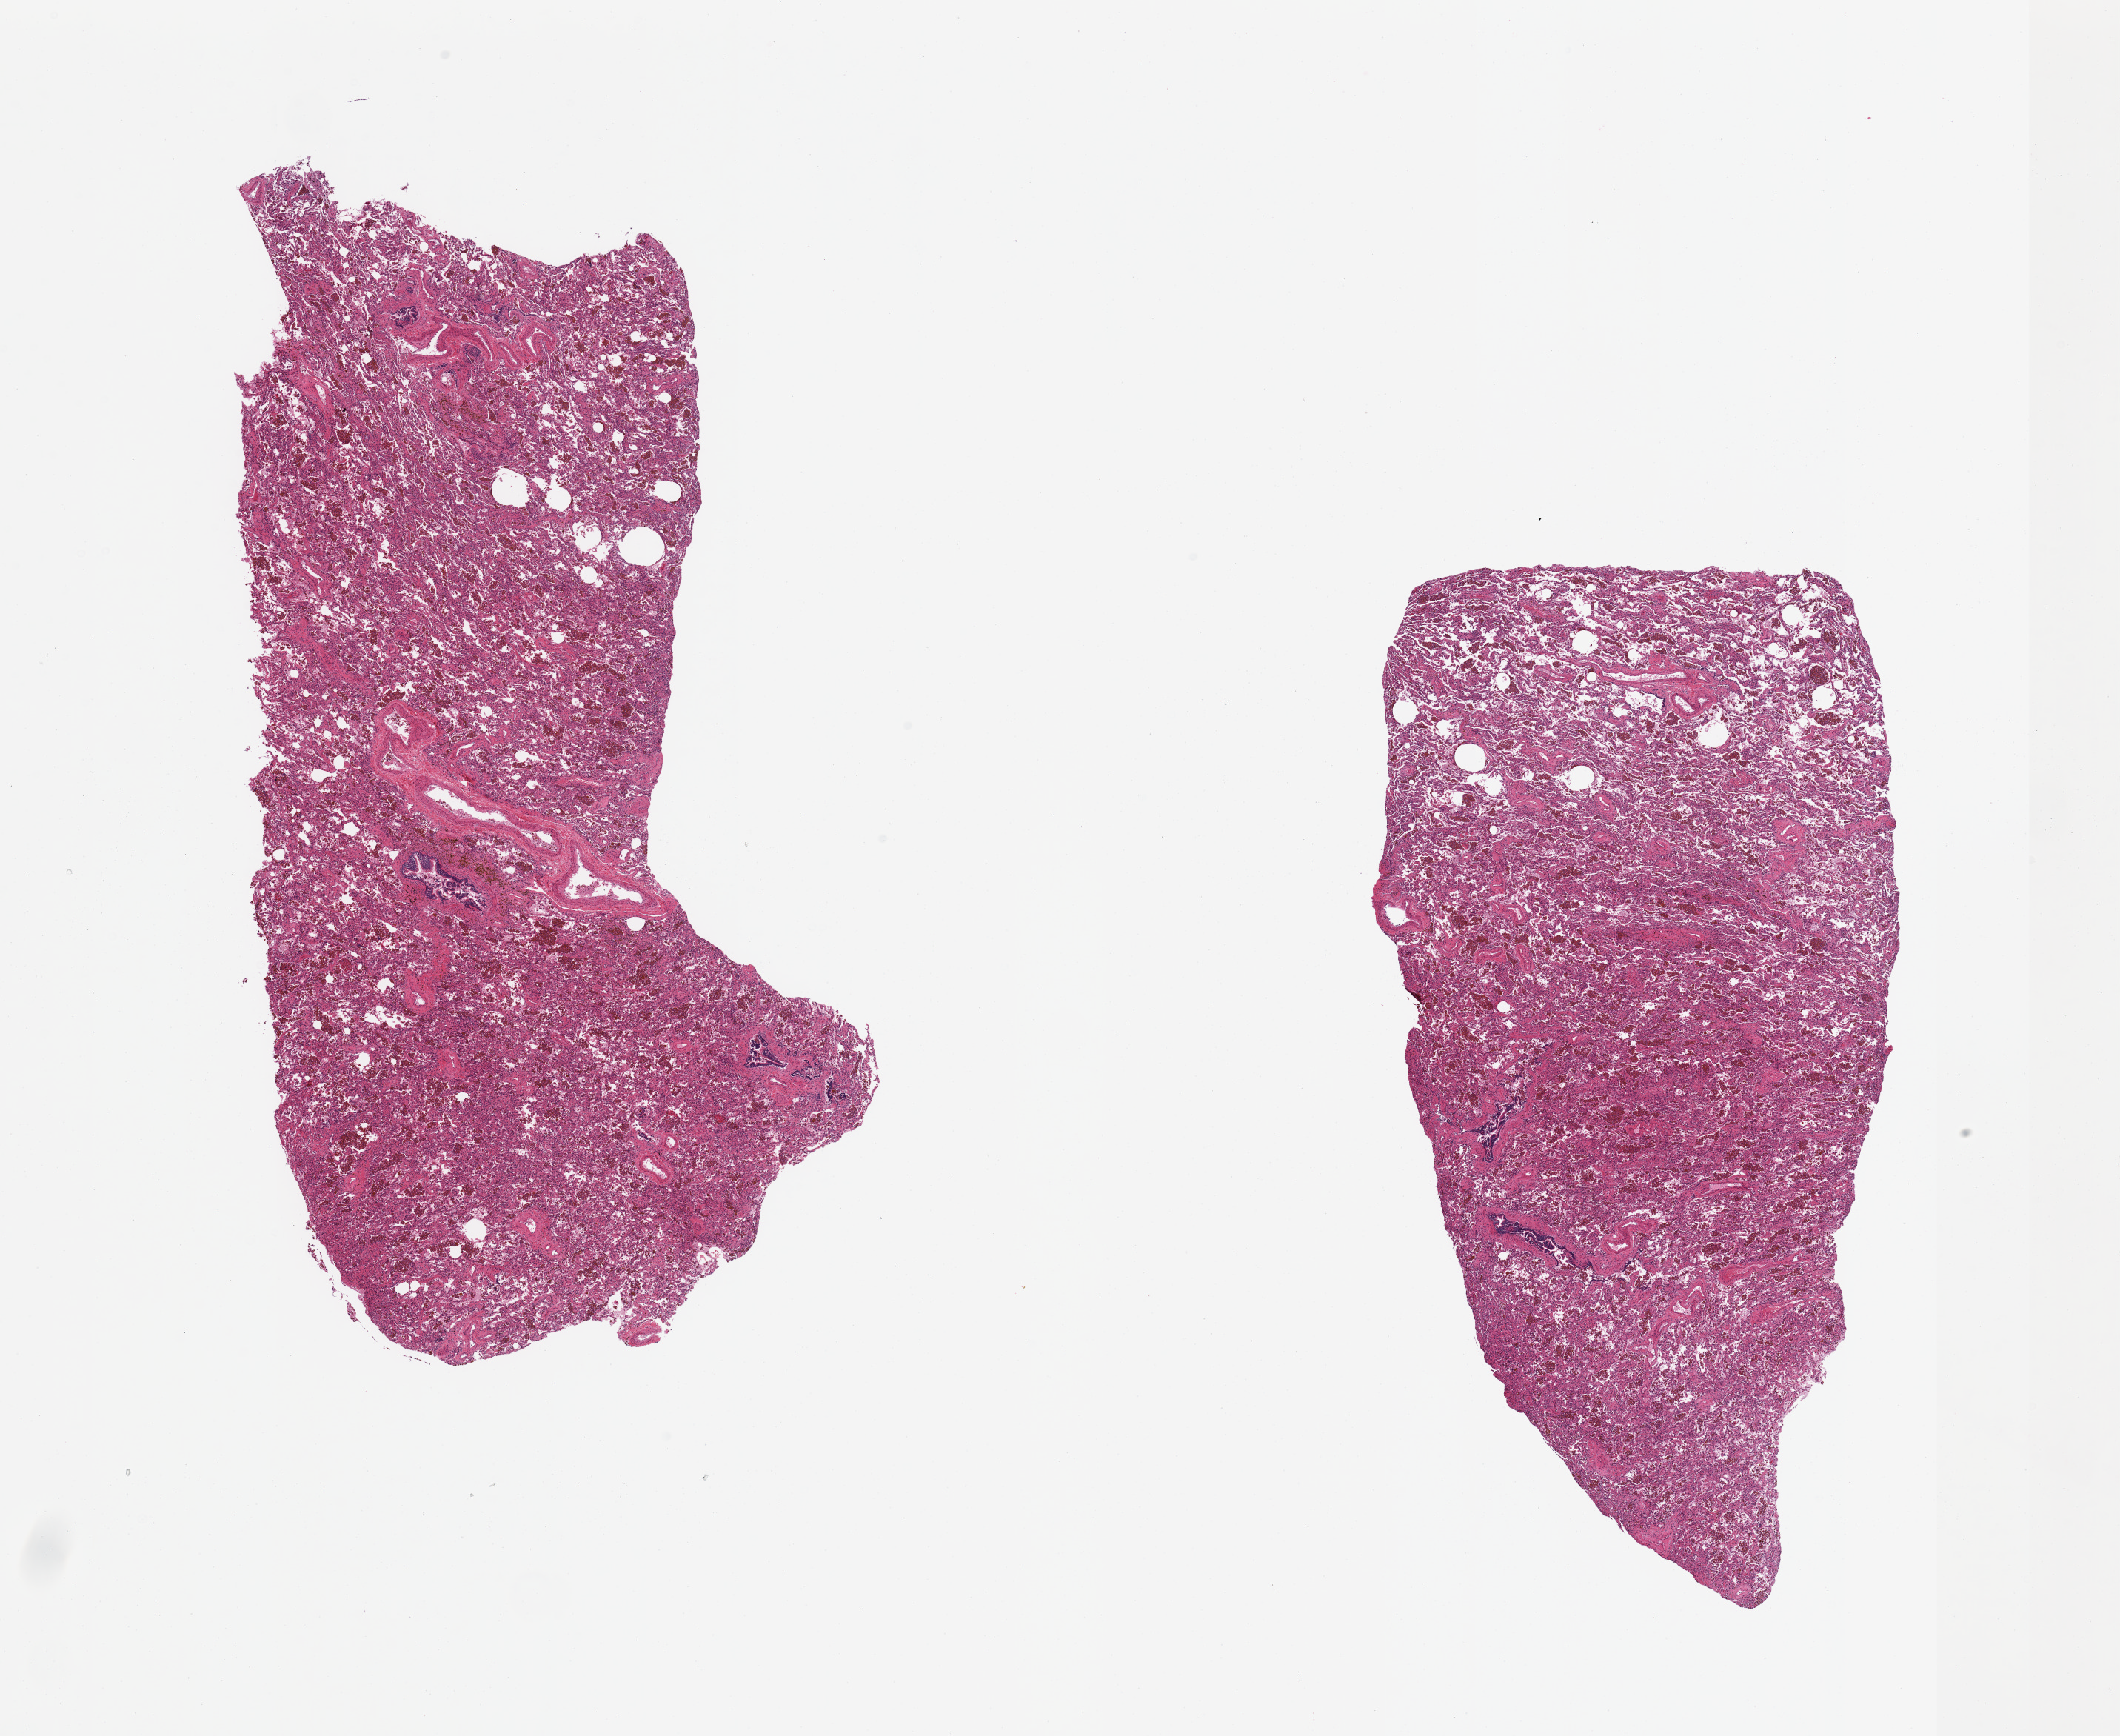
Whole-slide image, haematoxylin and eosin stain, brightfield, shown as a low-resolution overview of the whole scanned area (about 22.6 x 18.5 mm, slide scanned at 20x). PAXgene-fixed, paraffin-embedded tissue. Section of lung (target tissue). Donor tissue sample. Donor sex: male.
* review note (as recorded): 2 pieces, chronic congestion, mild edema, atalectasis